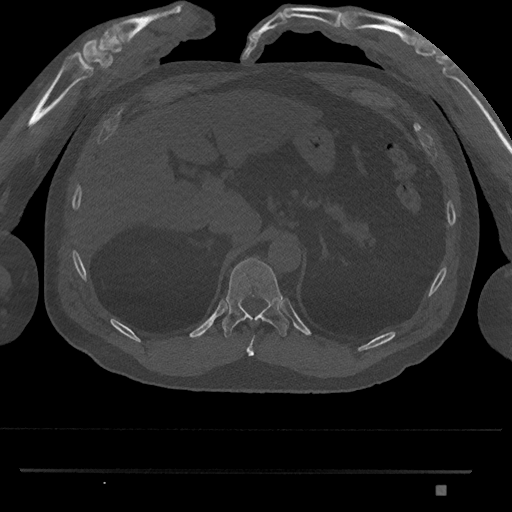
CT including the spine, one axial slice; position 955 of 1134 along the scan axis; 120 kVp; bone window (W 1800 / L 400 HU); 0.5 mm slice thickness; 512 × 512 image matrix. Male patient, age 65 years. Case-level facts recorded for this patient, not image findings: primary cancer: prostate.
Structures marked on this image (semi-automatically segmented with operator editing):
- T10 vertebra: bounding box <246,340,254,356> (left, top, right, bottom; pixels)
- T11 vertebra: <223,257,289,338>